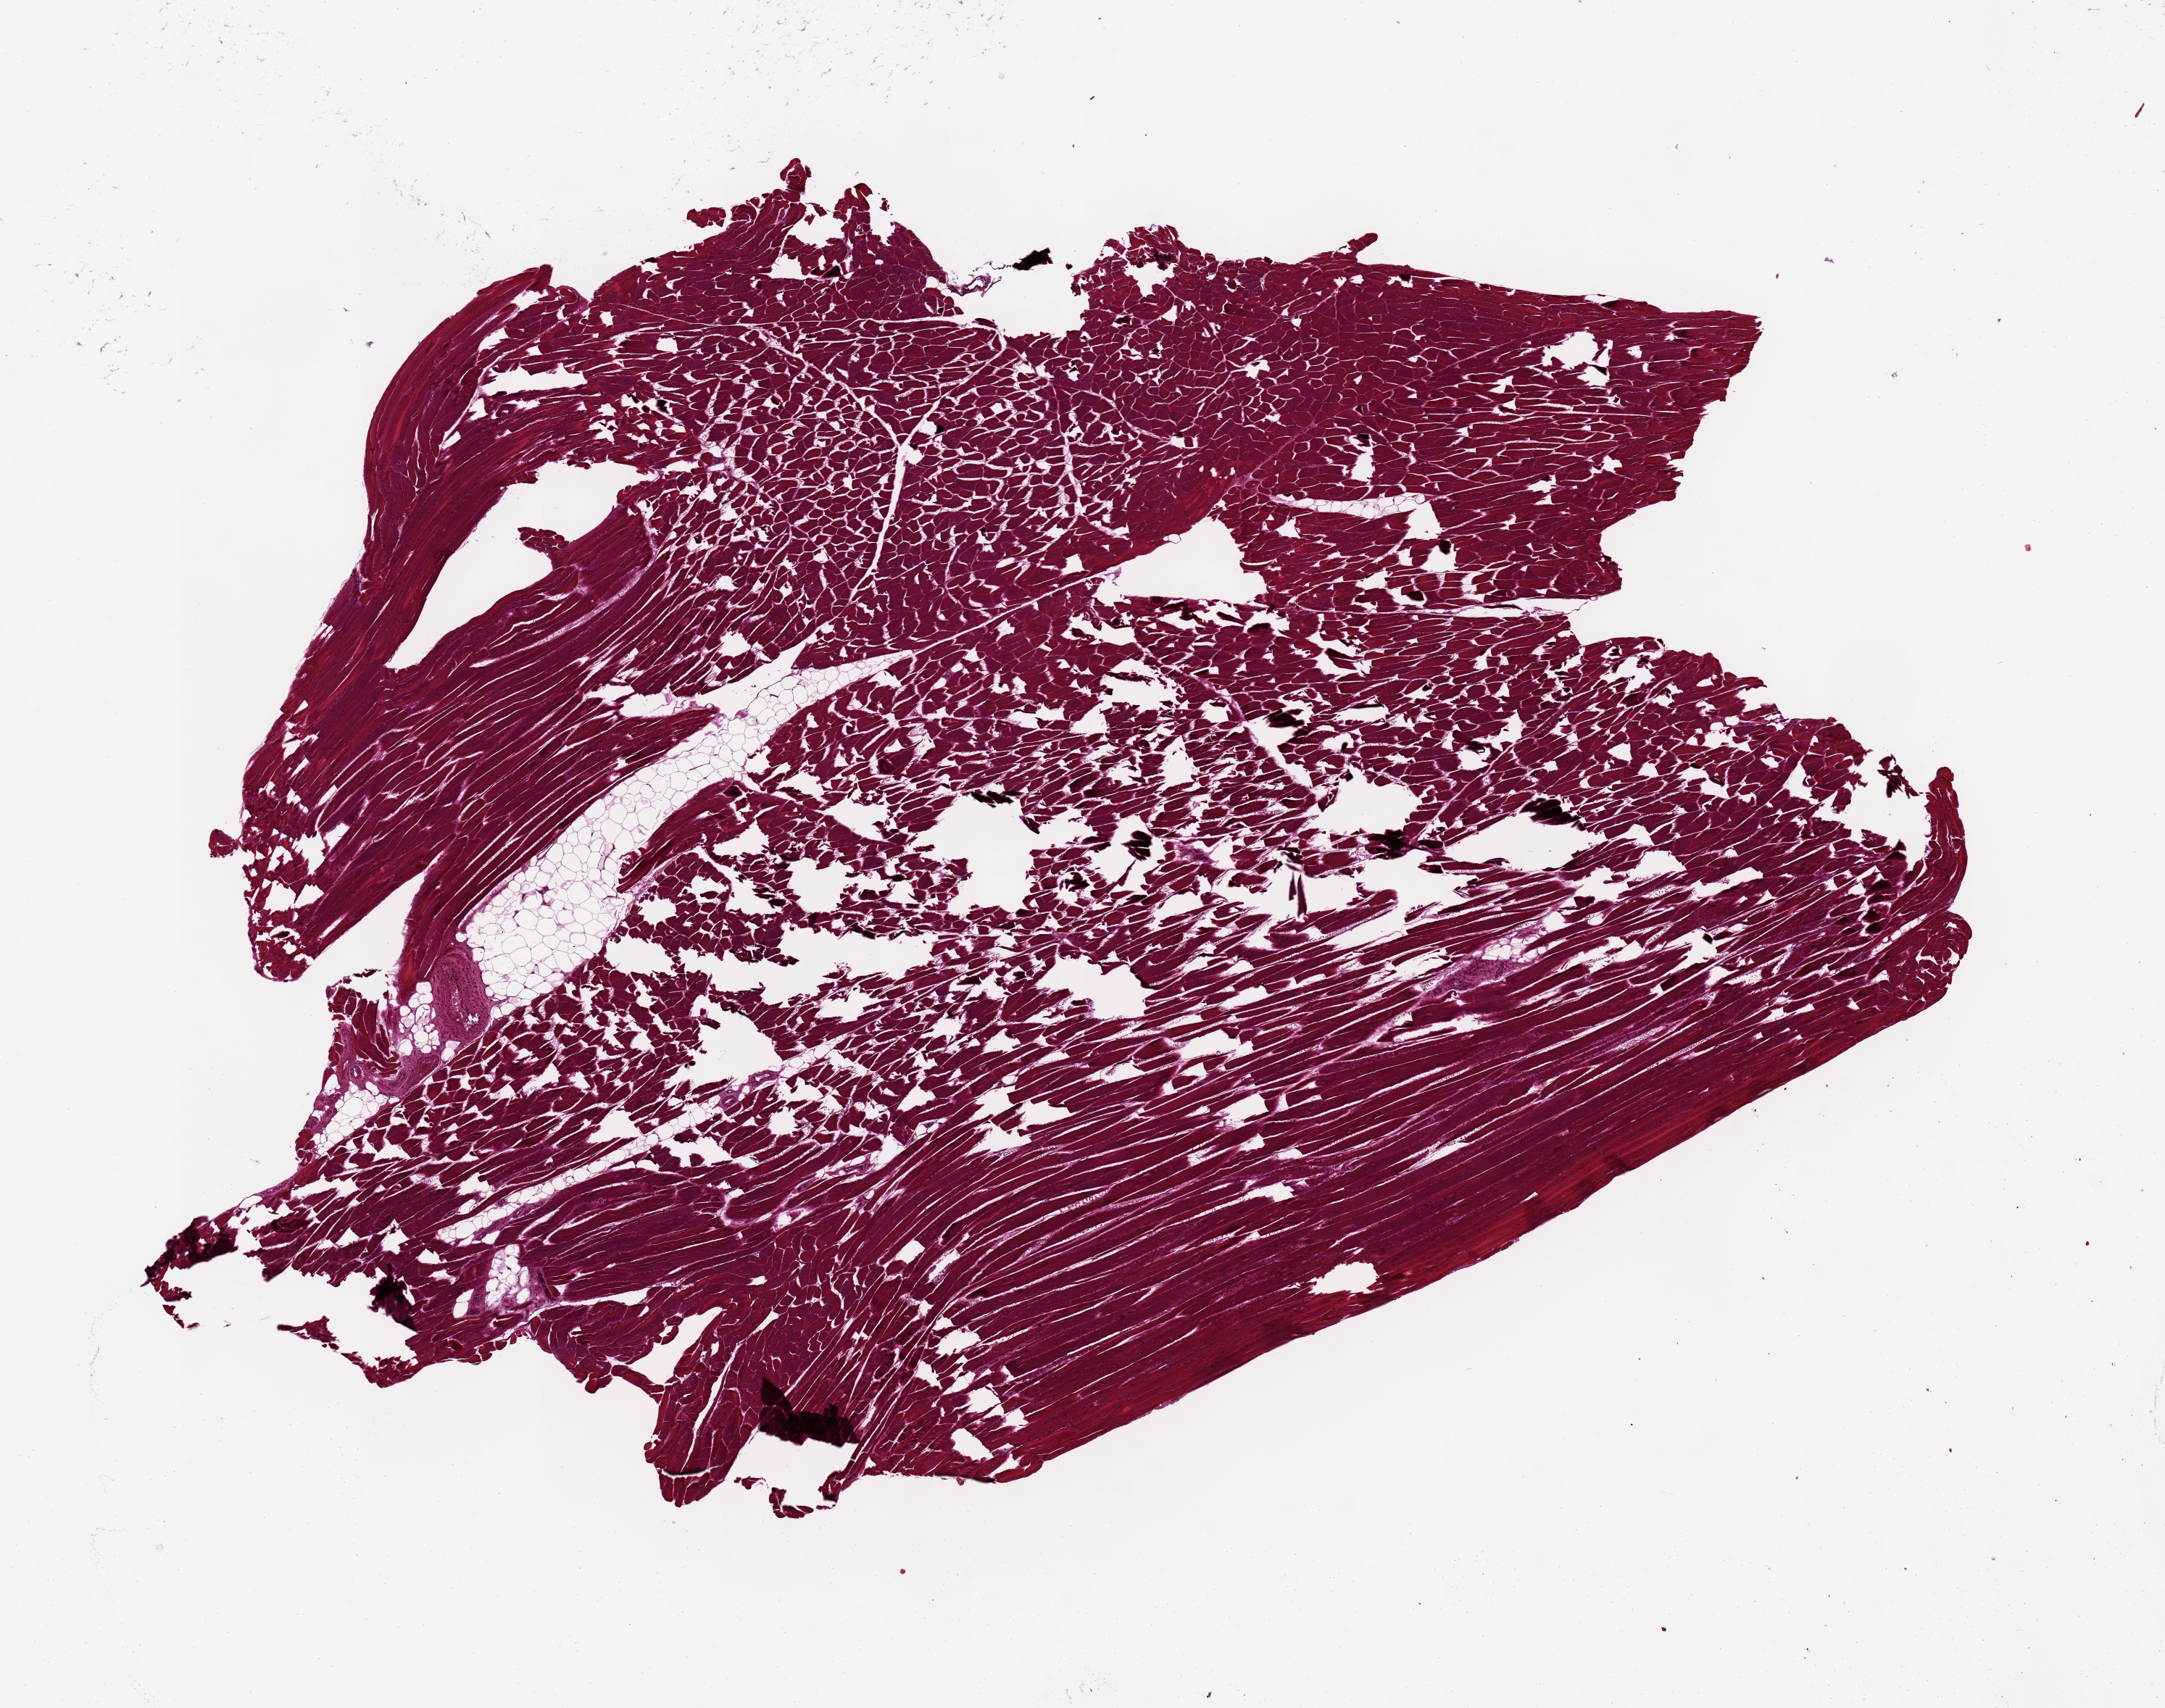
Digitized H&E-stained section, brightfield — whole scanned area (about 11.8 x 9.3 mm, acquisition: 20x scan) shown as a low-resolution overview, PAXgene-fixed, paraffin-embedded tissue, section of skeletal muscle (target tissue), donor tissue sample. Donor: male.
Pathologist's review note for this sample: Moderate tissue fracture.